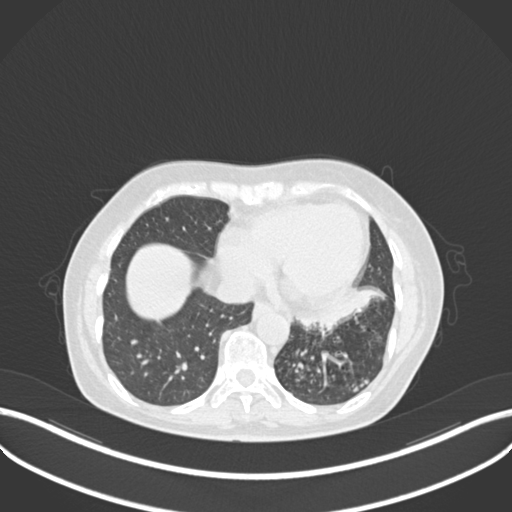
Chest CT, one axial slice; slice 81 of 270 in the series (ordered by position); 120 kVp; lung window (W 1500 / L -600 HU); 1 mm slice thickness; 512 × 512 image matrix, field of view 400 × 400 mm. Patient: female, 63 years. From the clinical record (not read from this slice): clinical TNM (as recorded): T1b N0 M0; histopathological grade: G2-3.
Structures marked on this image (bounding box drawn by a radiologist):
- lung tumour (recorded histology: adenocarcinoma): bounding box (x1, y1, x2, y2) in pixels: (291, 287, 388, 331)